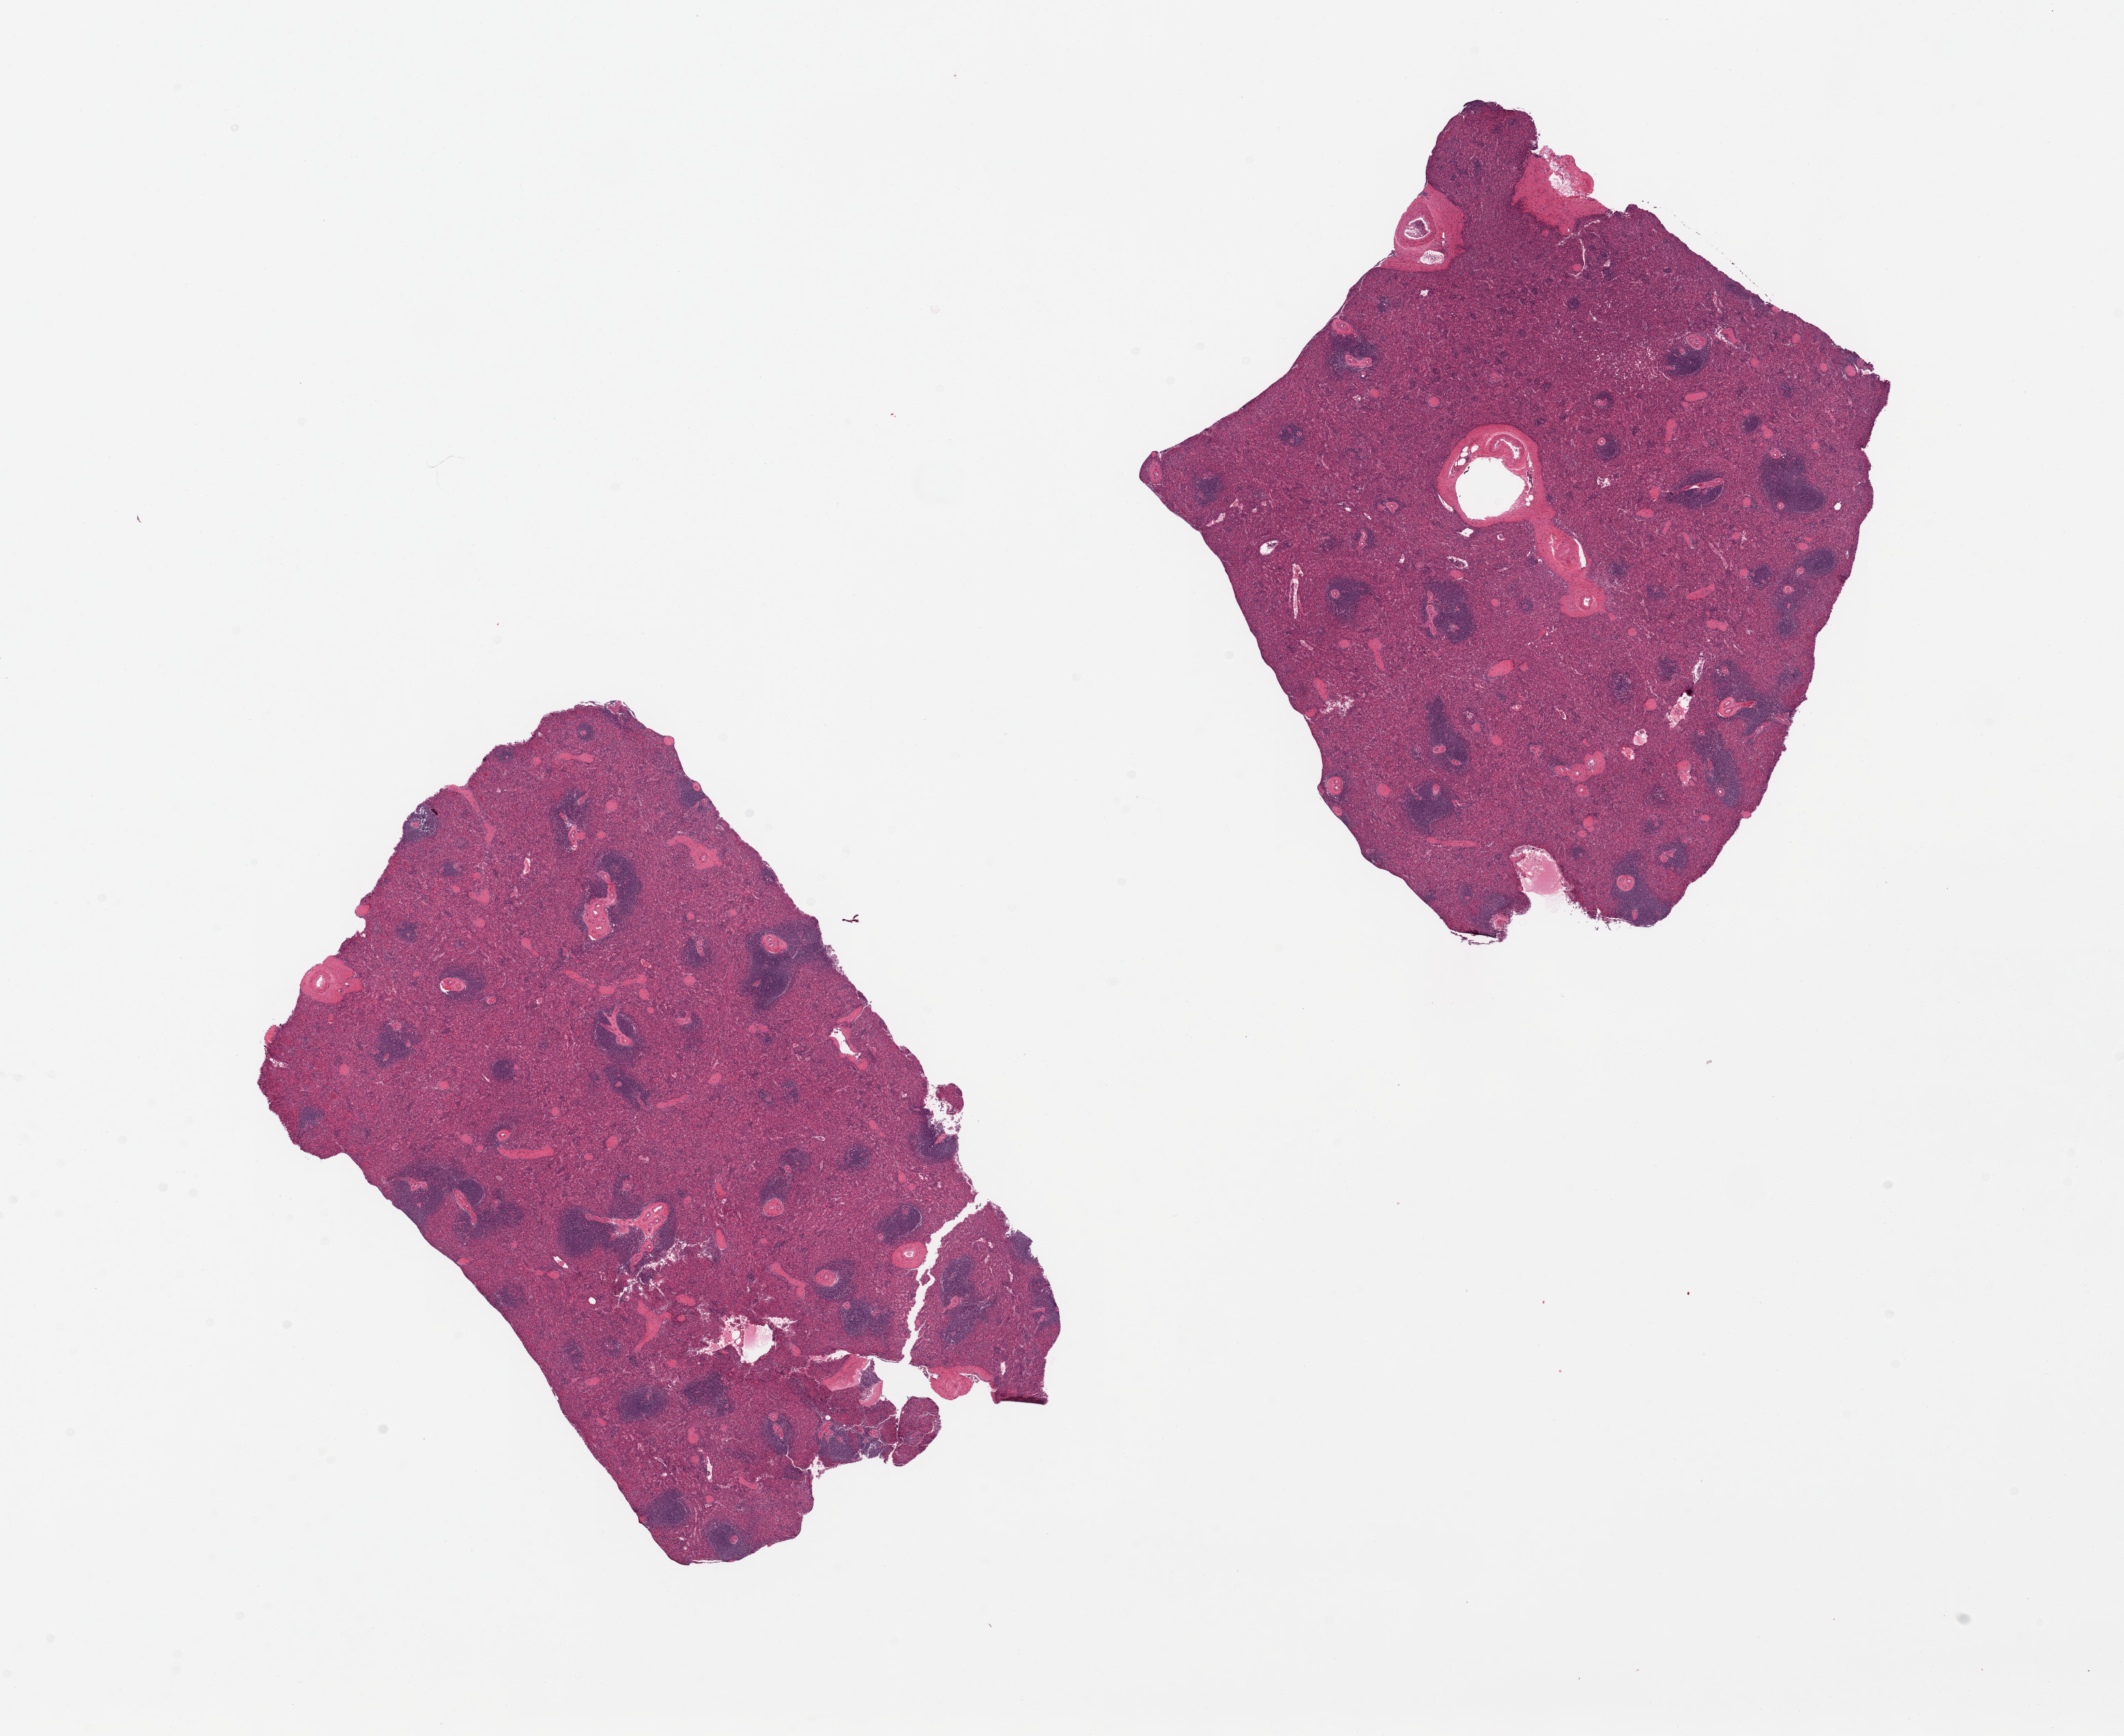
Haematoxylin and eosin whole-slide image, a low-resolution overview of the entire scanned area, about 24.6 x 20.1 mm, PAXgene-fixed paraffin-embedded (PFPE) section, sampled site (target tissue): spleen, tissue donor sample. Donor: female.
Pathologist's review note for this sample: 2 pieces.